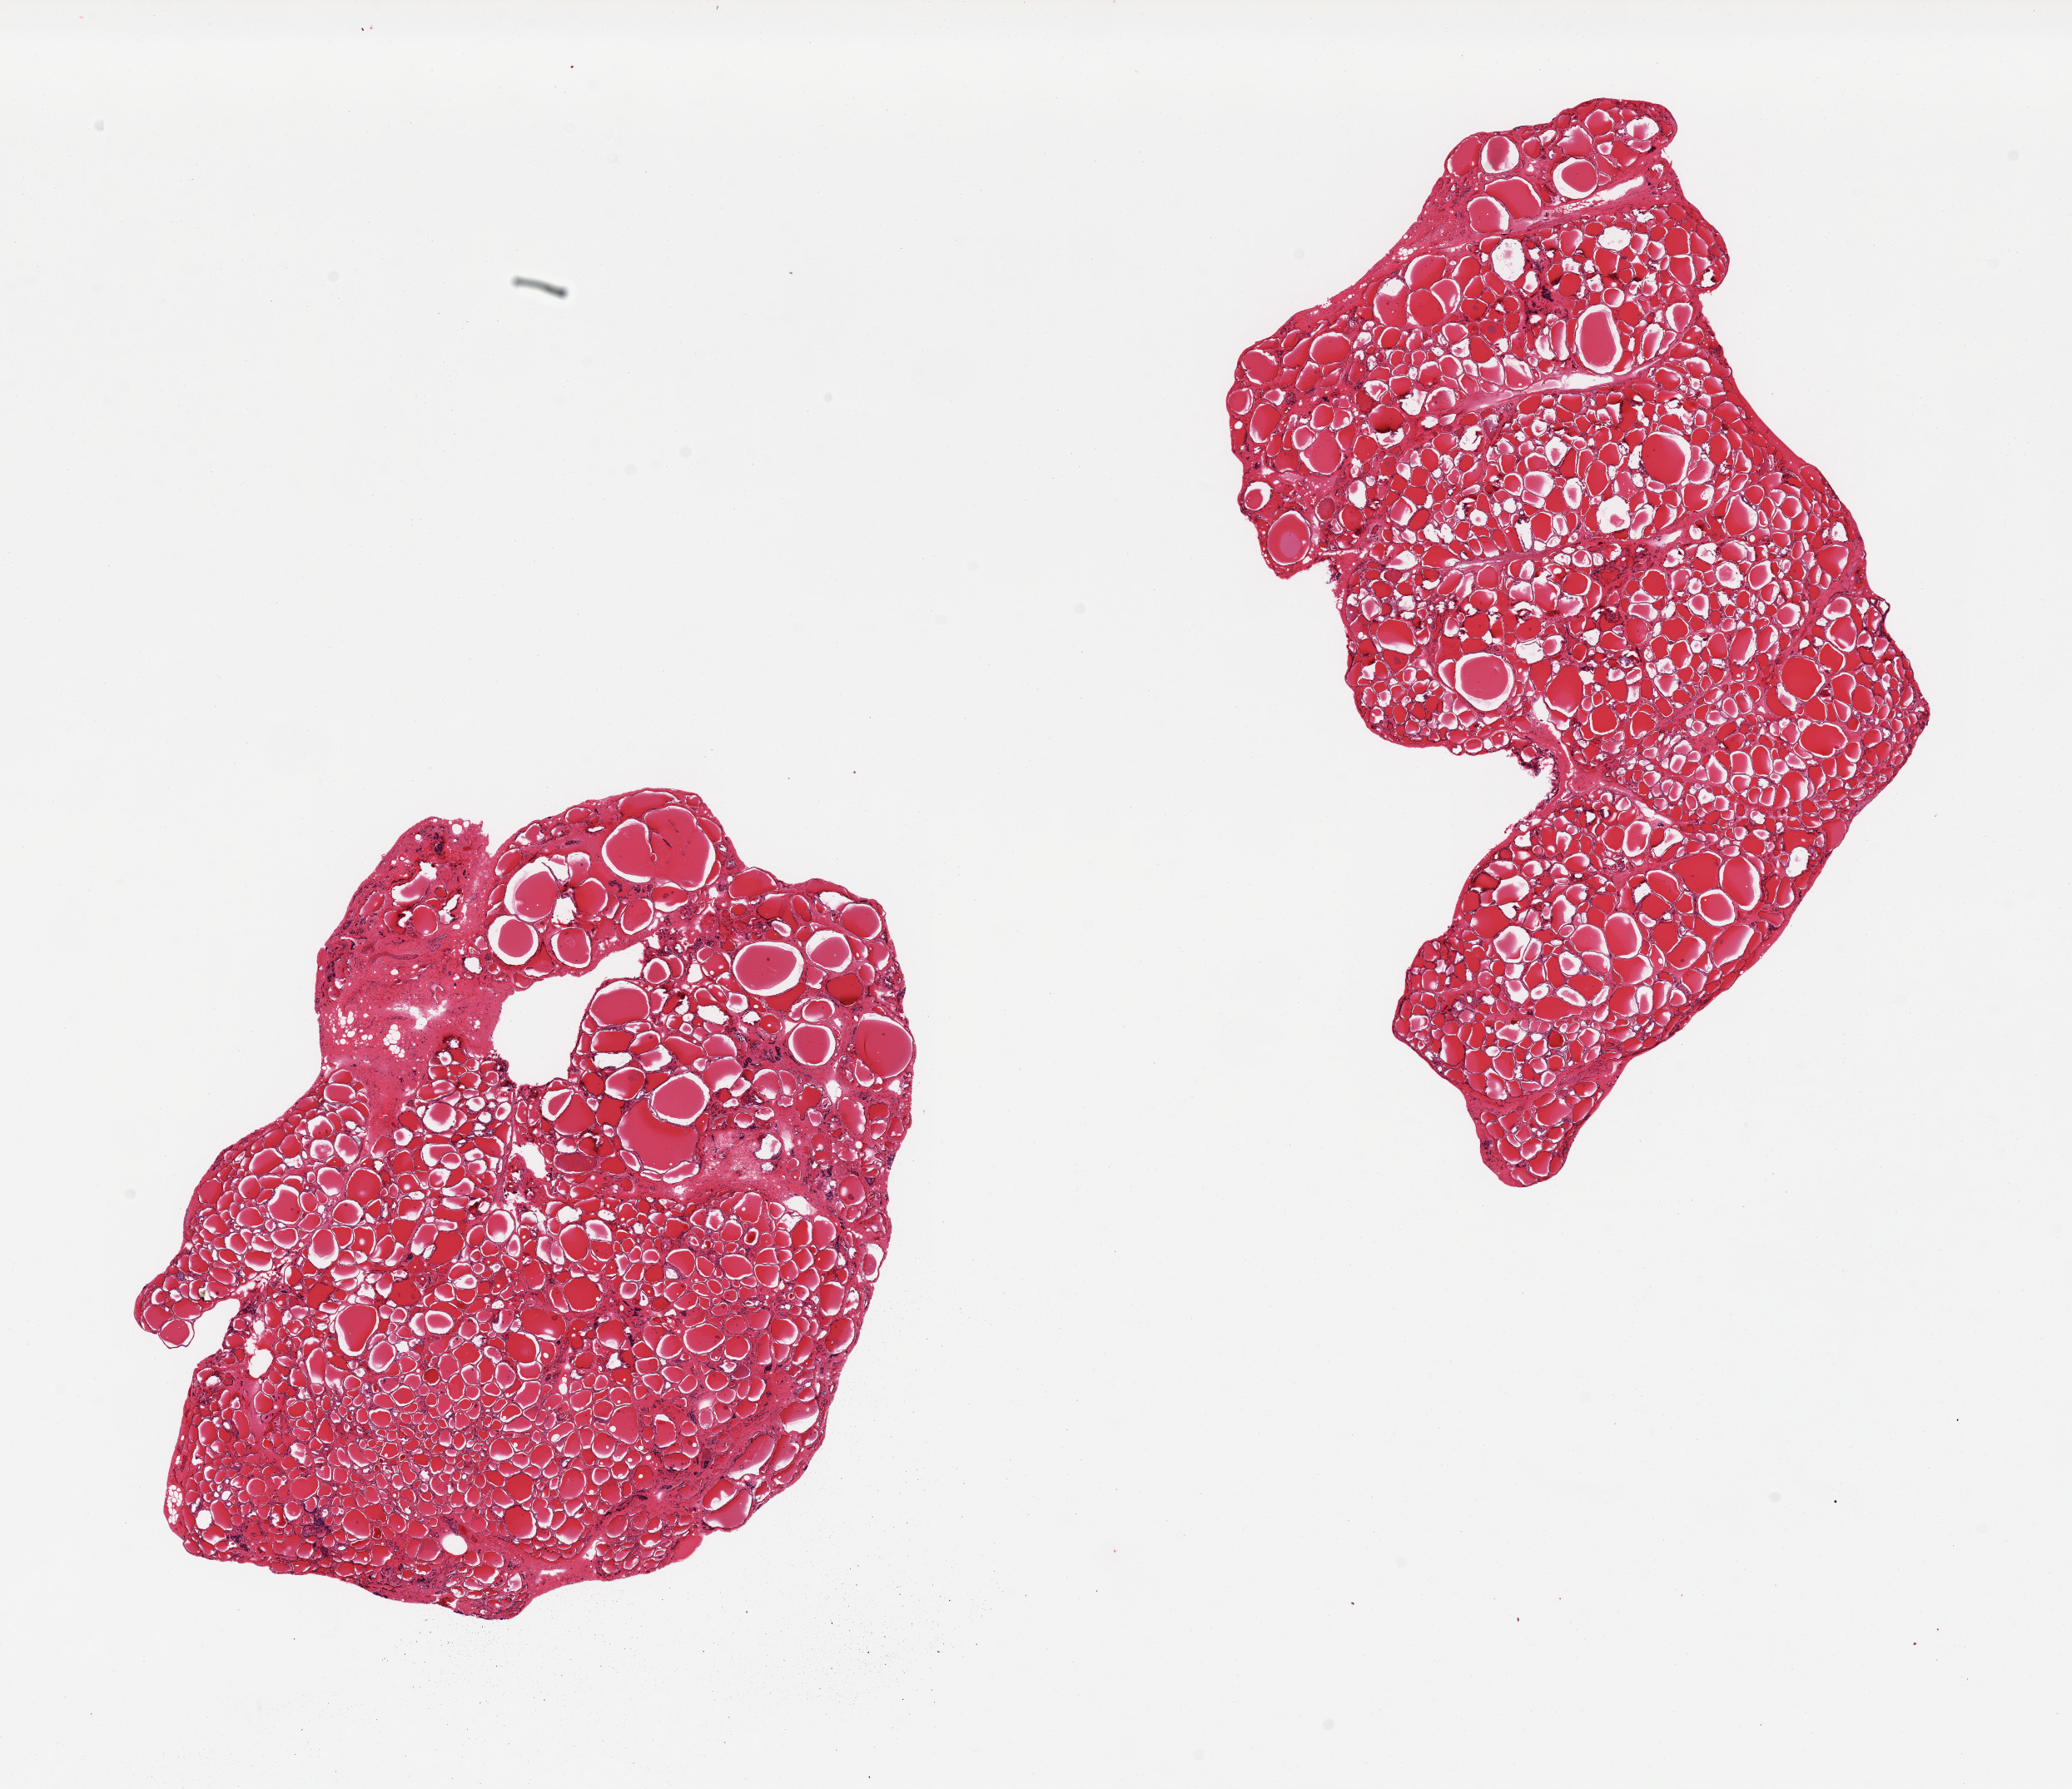
Digitized hematoxylin and eosin (H&E)-stained section — whole scanned area (about 19.7 x 17.0 mm) shown as a low-resolution overview. PAXgene-fixed, paraffin-embedded tissue. Section of thyroid (target tissue). Donor tissue sample. Male donor.
- reviewer comment on this tissue sample: 2 pieces